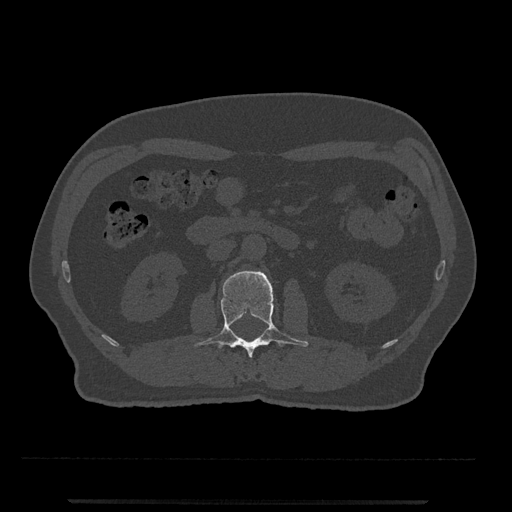
CT including the spine, one axial slice; slice 268 of 797 in the series (ordered by position); reconstruction kernel Br40s/3; 120 kVp; bone window (W 1800 / L 400 HU); 0.5 mm slice thickness; 512 × 512 image matrix, field of view 419 × 419 mm. Male patient, age 63 years. From the clinical record (not read from this slice): primary cancer: prostate.
Annotated regions visible in this slice (semi-automatically segmented with operator editing):
- L2 vertebra: box from (x=194, y=270) to (x=309, y=358) px